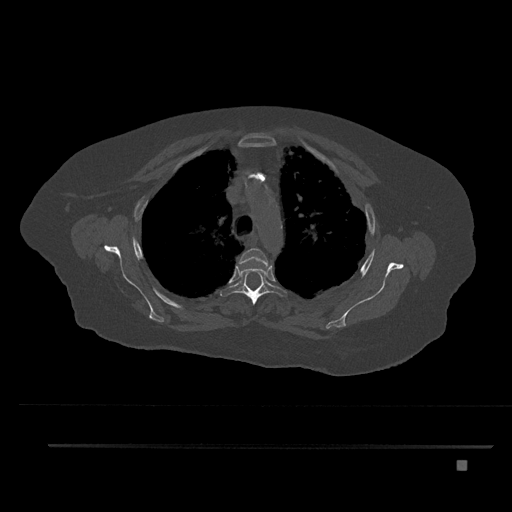
CT including the spine, one axial slice. Reconstruction kernel Br40s/3. 120 kVp. Bone window (W 1800 / L 400 HU). 0.5 mm slice thickness. 512 × 512 image matrix. Female patient, age 76 years. Case-level facts recorded for this patient, not image findings: primary cancer: lung; vertebrae with lytic lesions (as recorded): T11, L3.
Outlined on this slice (semi-automatic segmentation, software-assisted and operator-edited):
- T3 vertebra: bounding box <239,248,270,268> (left, top, right, bottom; pixels)
- T4 vertebra: <220,258,288,305>